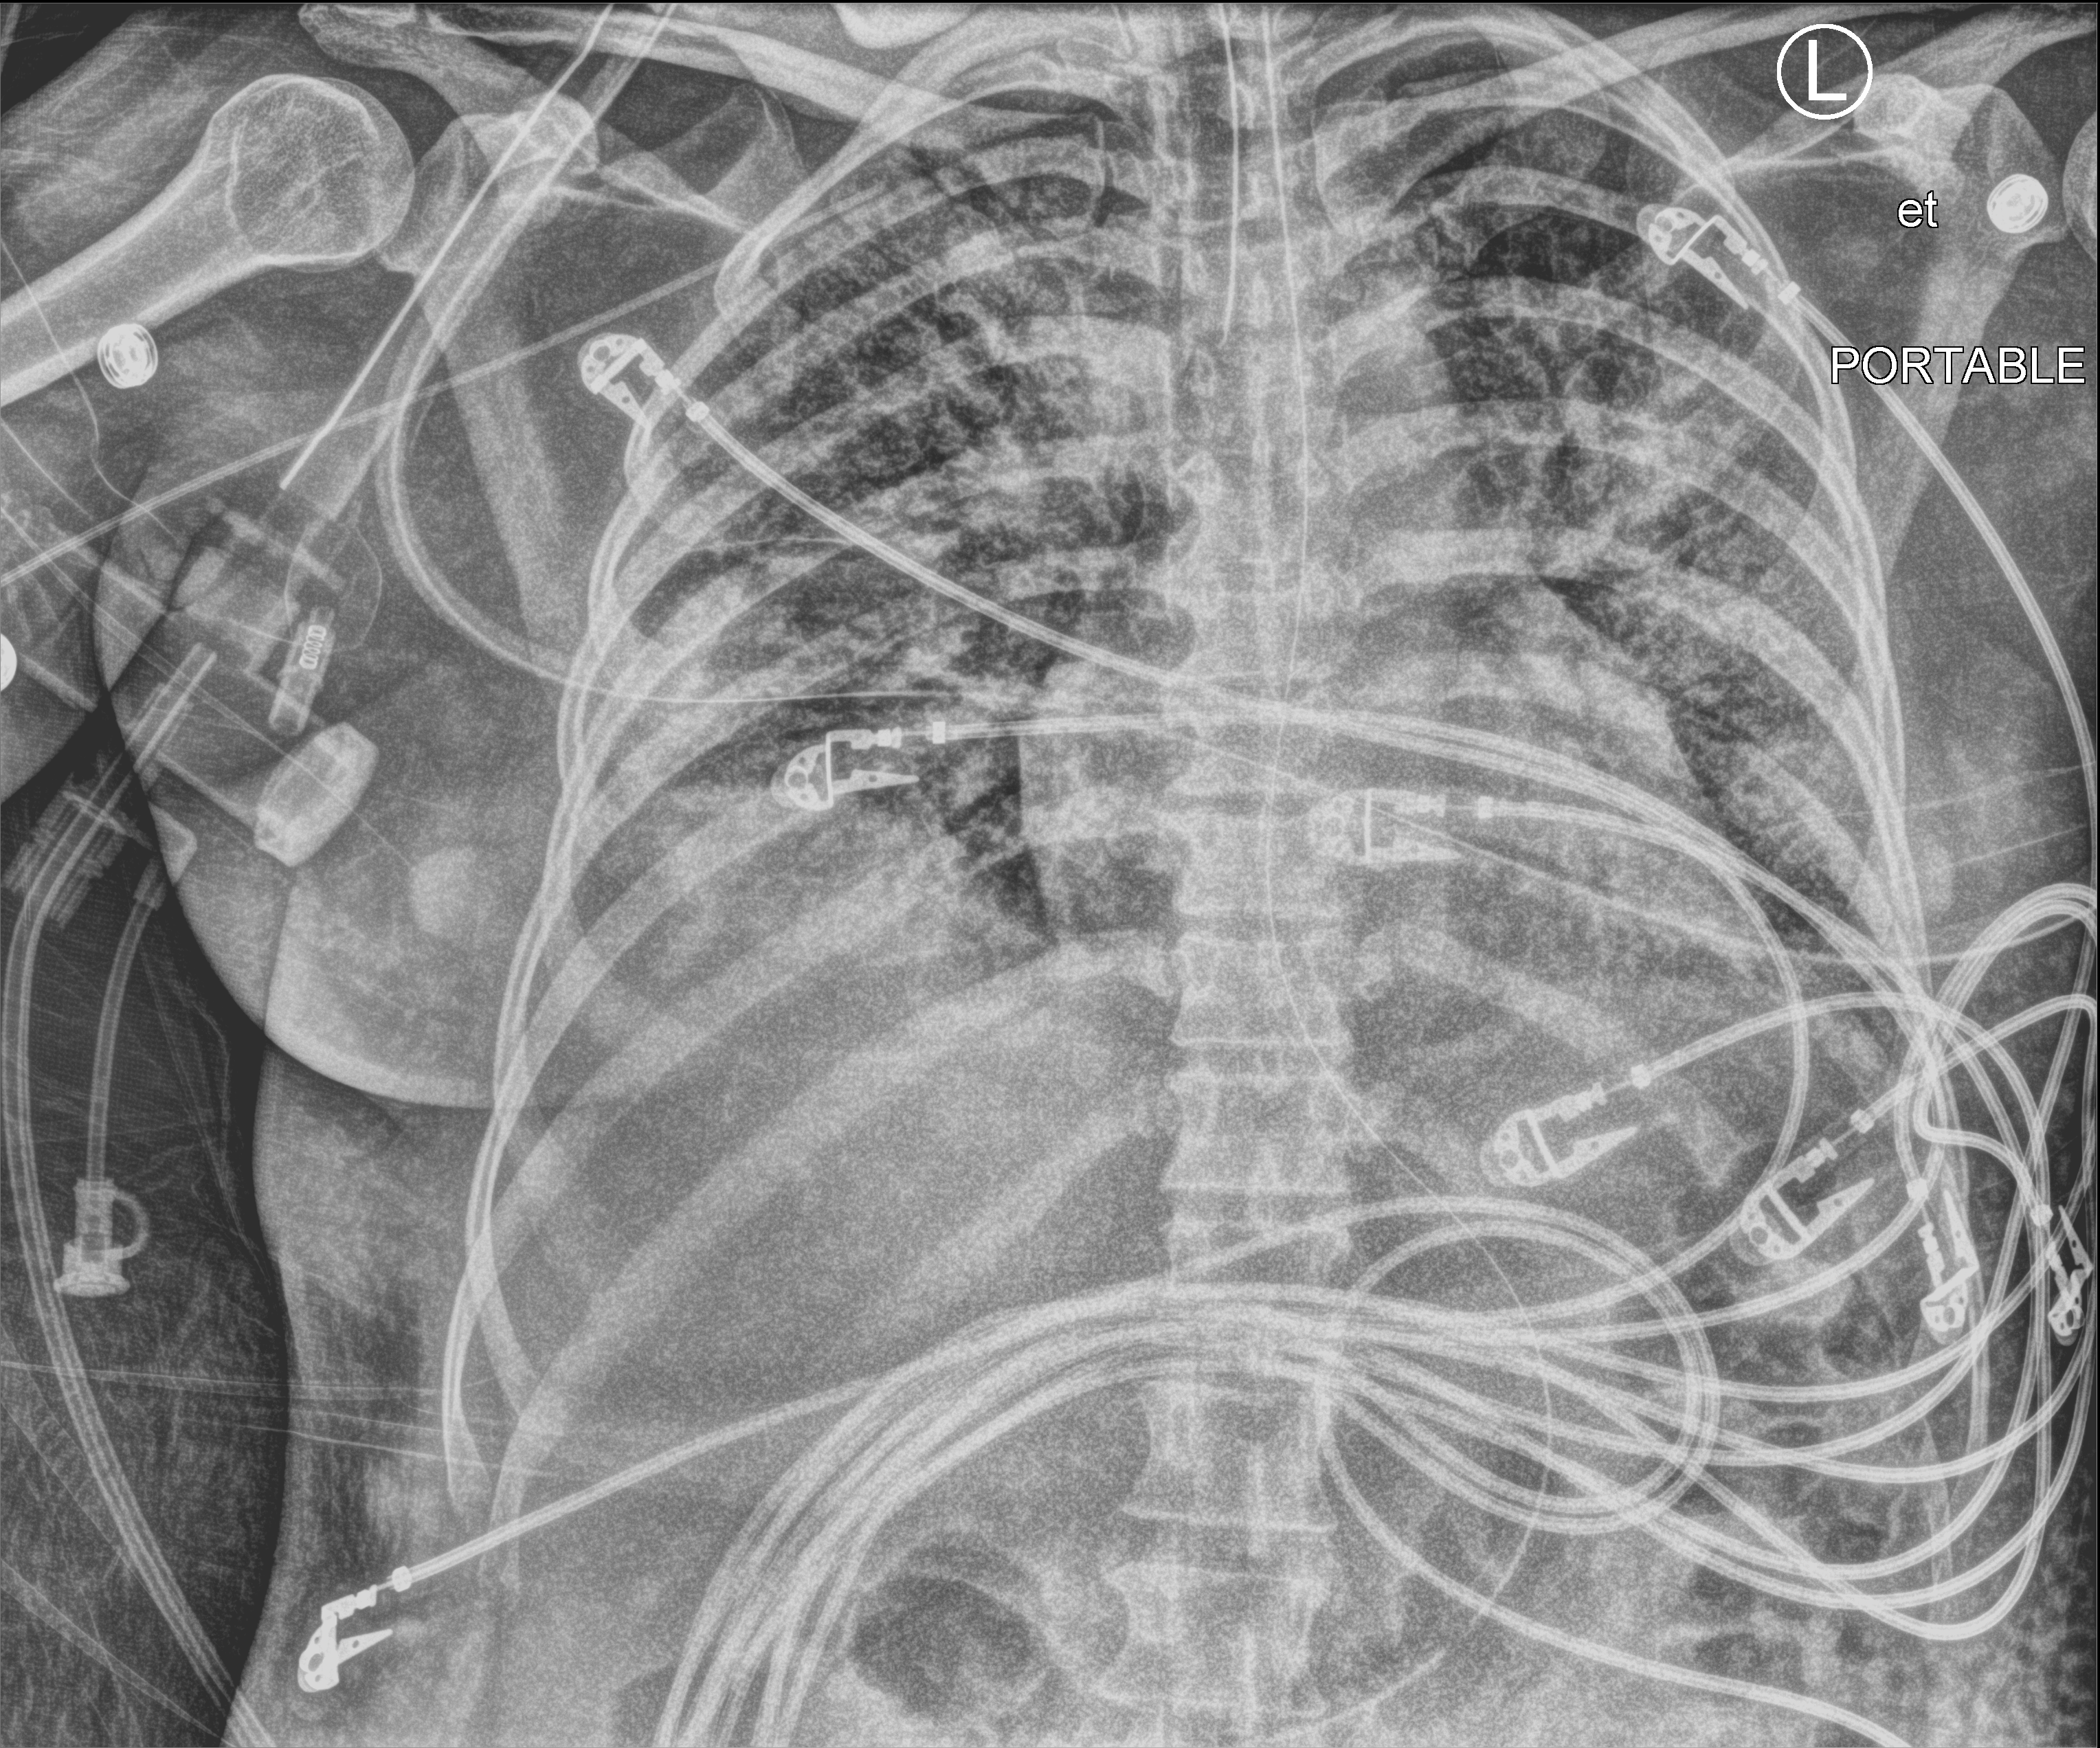
Portable chest radiograph; anteroposterior (AP) projection. Patient hospitalised with COVID-19; female, aged 18–59 years.
Admission-level facts for this patient (not findings on this image; timing relative to this image not recorded):
- admitted to intensive care during this hospital stay: yes
- length of hospital stay: 71 days